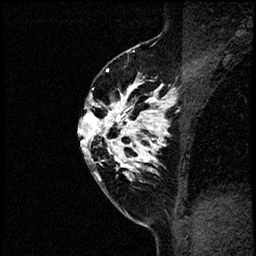
Breast MRI (dynamic contrast-enhanced), one sagittal slice; position 39 of 60 along the scan axis; dynamic contrast-enhanced study with each time point stored as its own series, time point 2 of 4 at this slice position (early post-contrast, ordered by acquisition time); 1.5 T; TE 4.2 ms, TR 17.6 ms; 2 mm slice thickness; 256 × 256 image matrix. Patient: female, 40 years. Case-level facts recorded for this patient, not image findings: setting: breast cancer imaged before/during neoadjuvant chemotherapy; receptor status: HER2-positive.
Structures marked on this image (semi-automatically segmented with operator editing):
- analysis volume of interest (the breast-tissue region the enhancement analysis was run in; not a lesion): bounding box (x1, y1, x2, y2) in pixels: (79, 56, 197, 205)
- tumour enhancement mask (voxels above the 100 % enhancement threshold inside the analysis volume of interest): (79, 68, 197, 181)